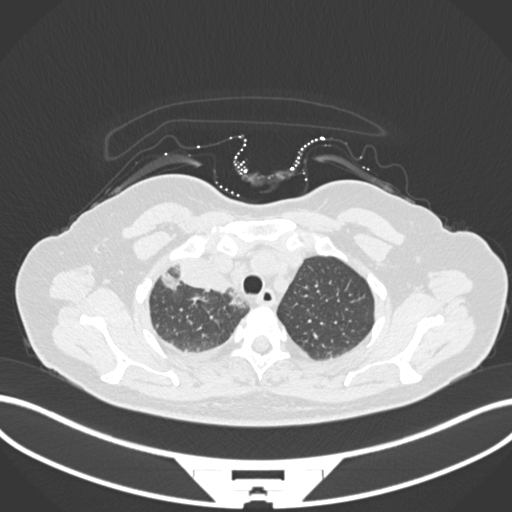
Chest CT, one axial slice. Position 138 of 172 along the scan axis. 120 kVp. Lung window (W 1500 / L -600 HU). 1 mm slice thickness. 512 × 512 image matrix, field of view 400 × 400 mm. Female patient, age 52 years. Case-level facts recorded for this patient, not image findings: clinical TNM (as recorded): T3 N1 M1.
Structures marked on this image (rectangle marked by the reading radiologist):
- lung tumour (recorded histology: adenocarcinoma): bounding box [x1, y1, x2, y2] px = [159, 260, 235, 296]